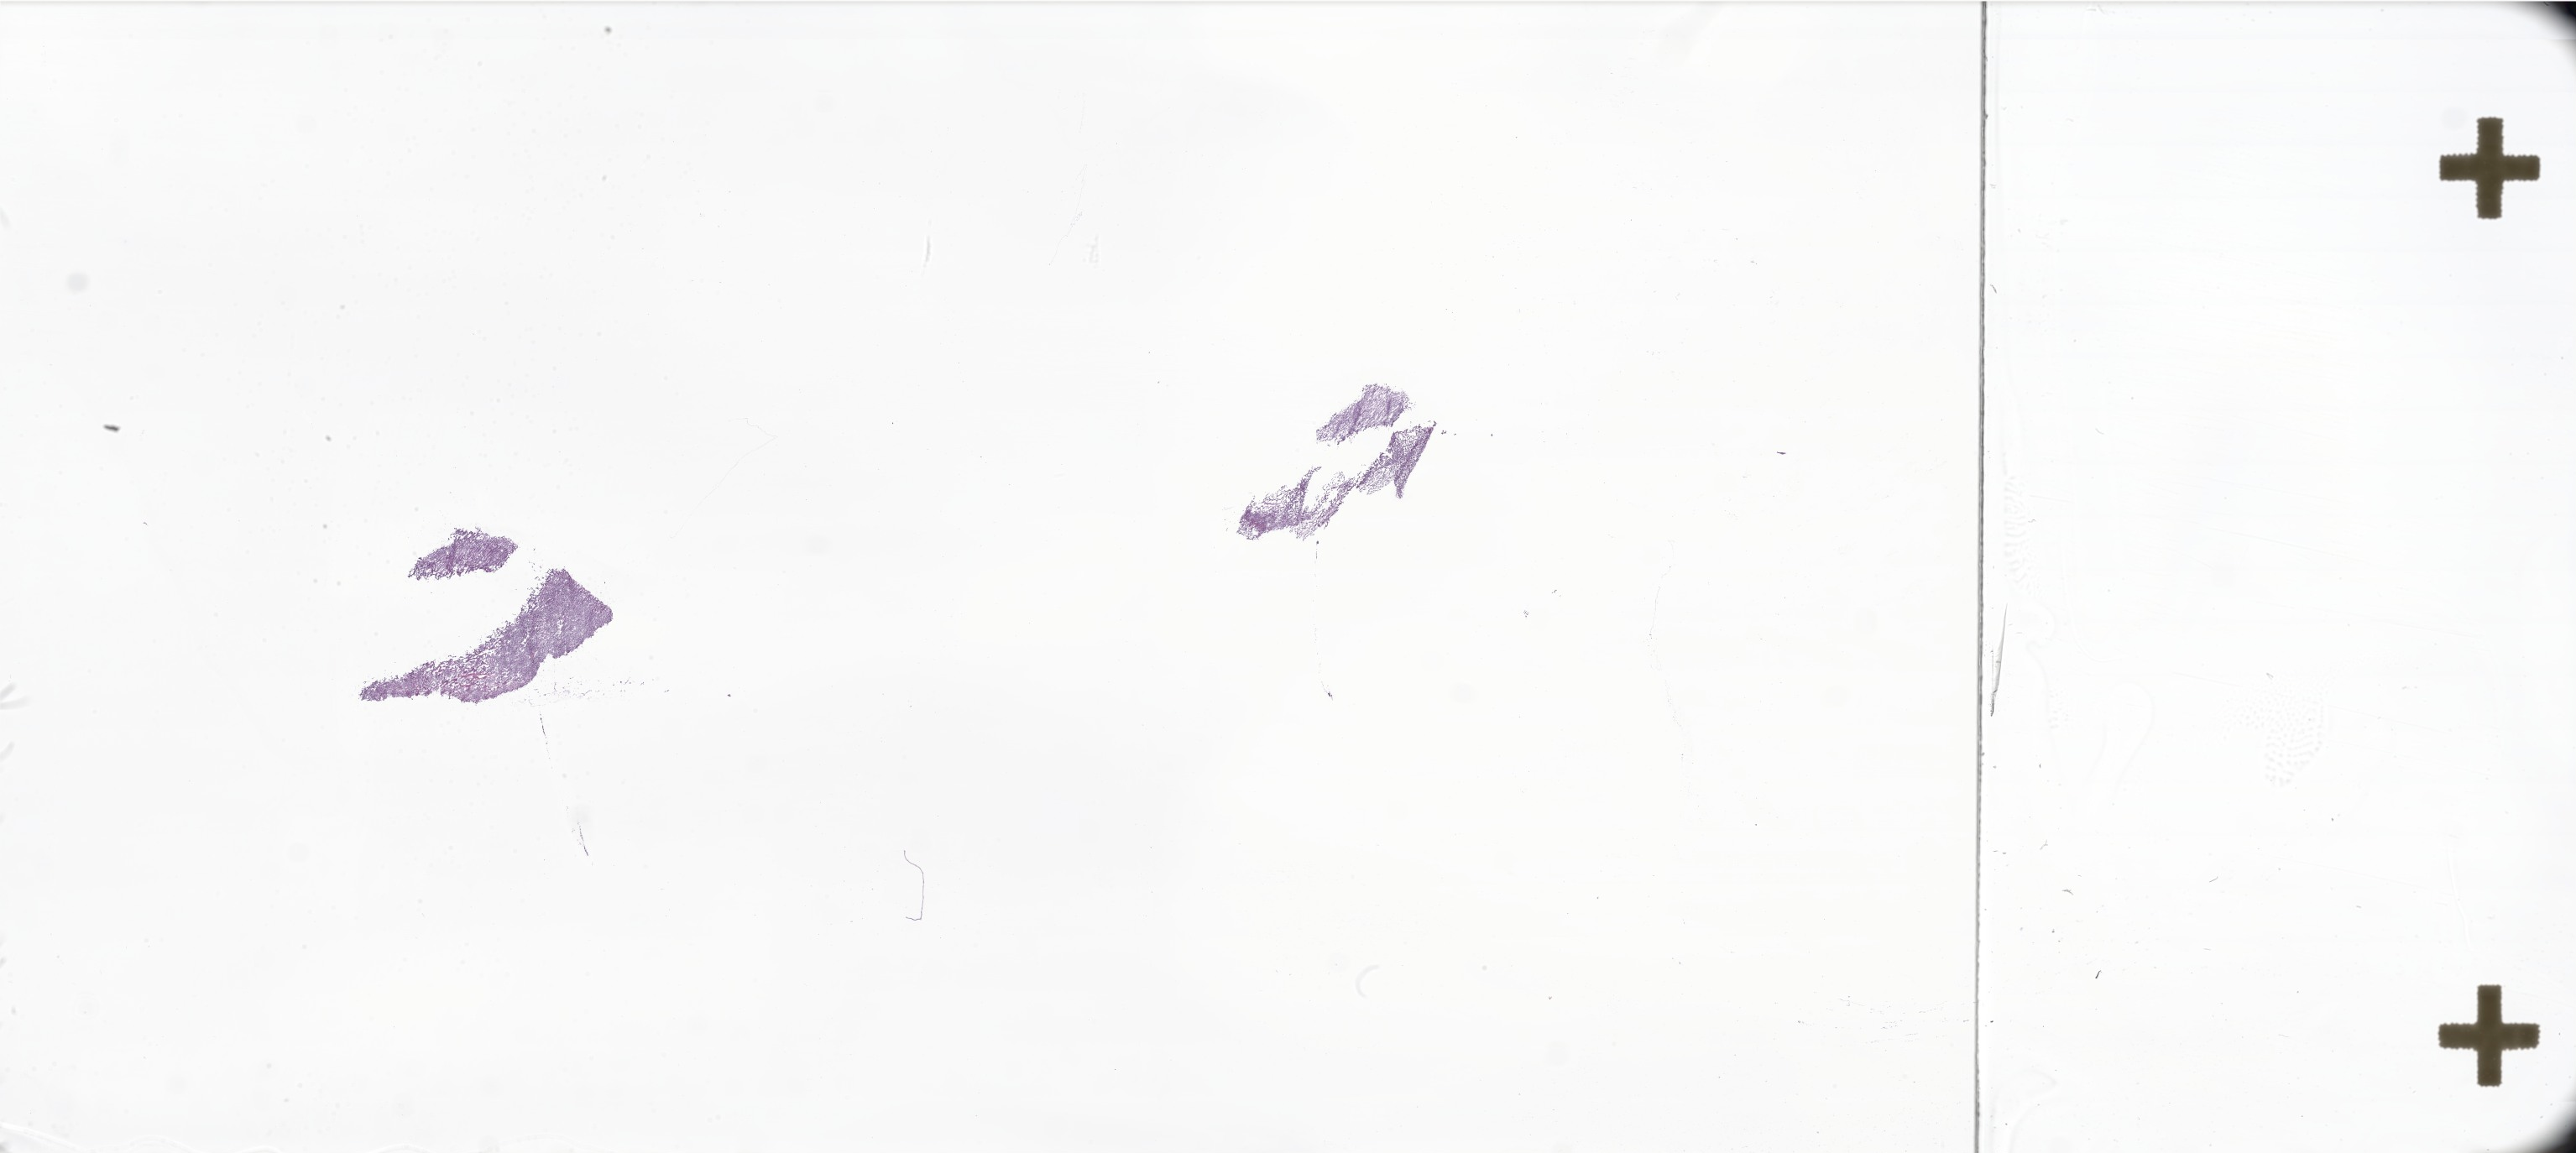
Whole-slide image, H&E stain of tumor tissue from the brain, shown as a low-resolution overview of the whole scanned area (about 51.8 x 23.2 mm), frozen section. Patient male; age 34 months.
Diagnosis (ICD-O-3 morphology term): Ependymoma, NOS.